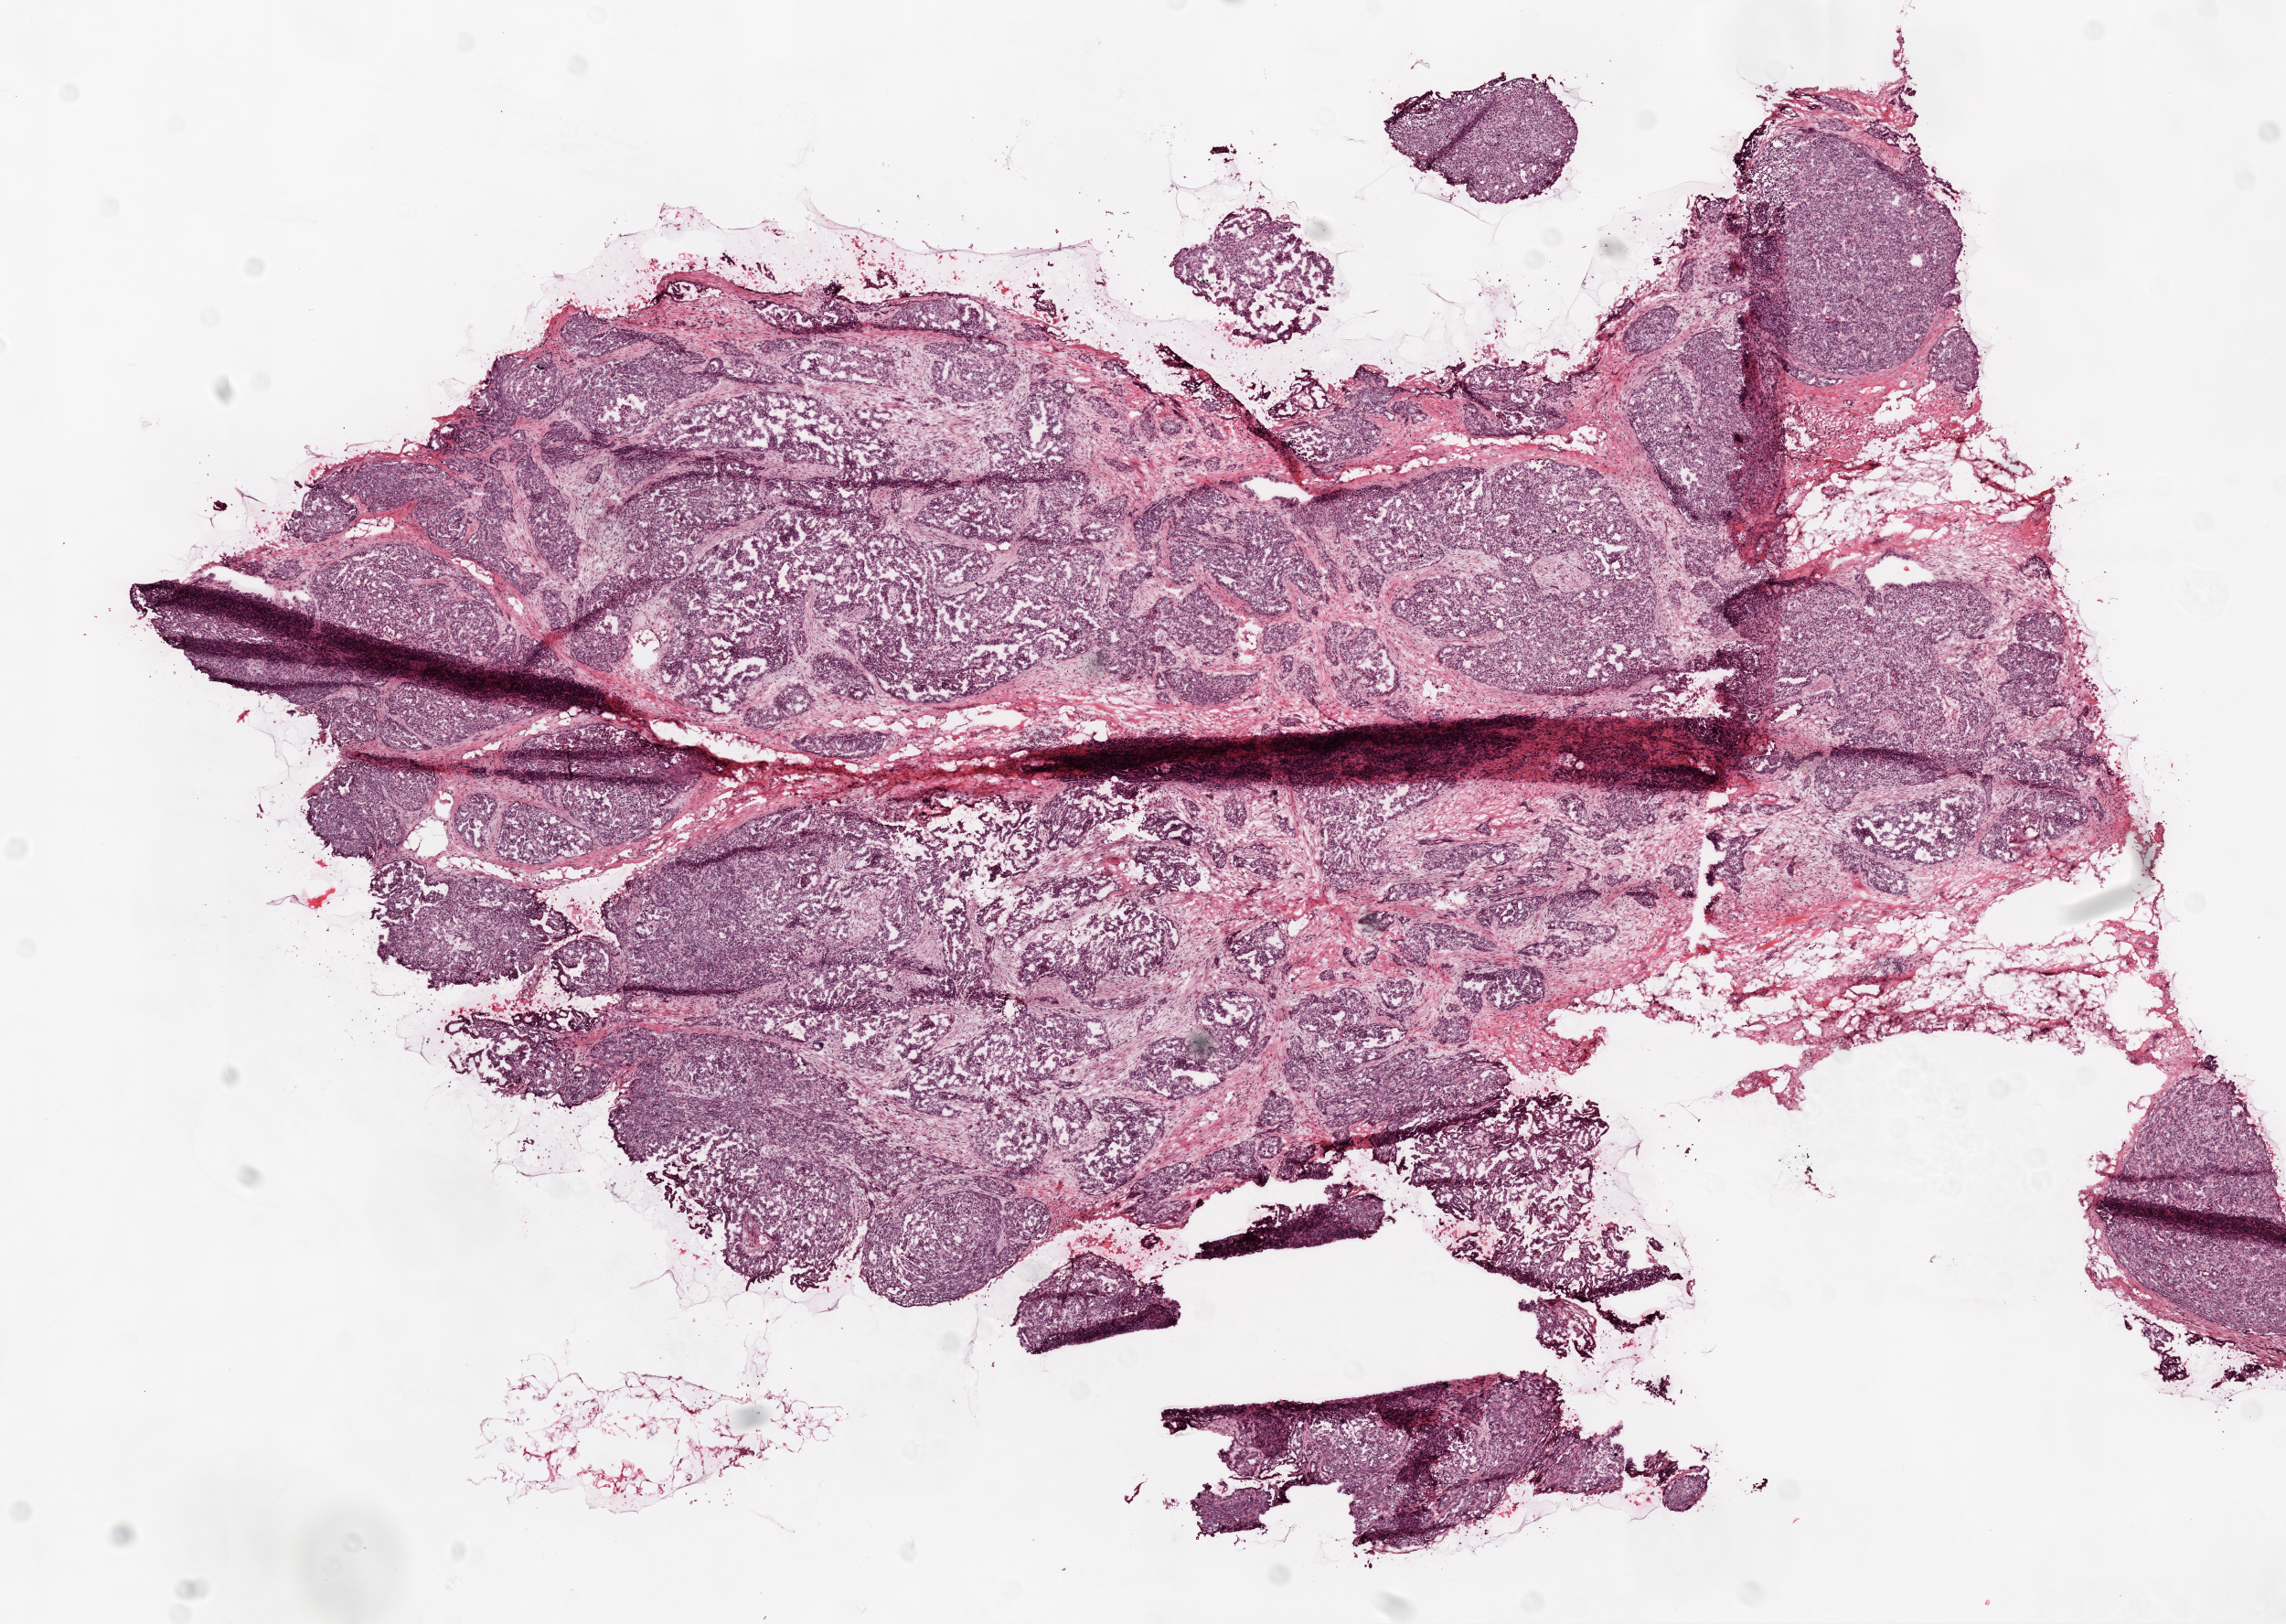
Digitized H&E tissue section (whole slide), shown as a low-resolution overview of the whole scanned area (about 10.0 x 7.1 mm, acquisition: 20x scan); frozen section from the top of the tissue portion; primary tumour sample from the ovary. Female patient; age at initial diagnosis 63 years. Histologic grade: G3 (poorly differentiated). Slide review estimates, as recorded: tumour cells 75%, tumour nuclei 90%, normal cells 0%, stromal cells 25%, necrosis 0%. Inflammatory infiltration, as recorded: lymphocyte infiltration 5%.
Diagnosis: Serous cystadenocarcinoma, NOS. FIGO stage: IIIC.